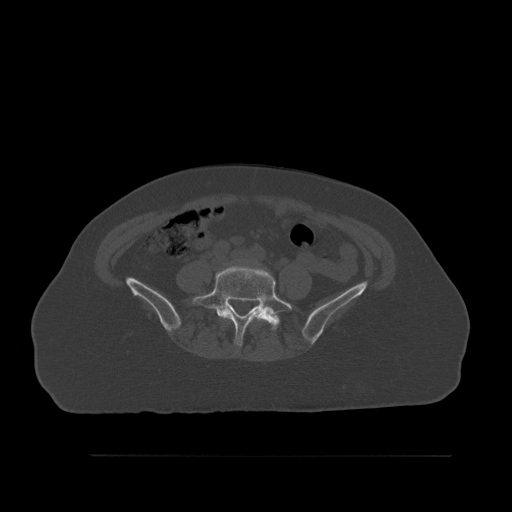
CT including the spine, one axial slice; slice 191 of 527 in the series (ordered by position); bone window (W 1800 / L 400 HU); 1.5 mm slice thickness; 512 × 512 image matrix, field of view 470 × 470 mm. Female patient, age 73 years. From the clinical record (not read from this slice): primary cancer: breast.
Annotated regions visible in this slice (semi-automatically segmented with operator editing):
- L4 vertebra: bounding box (x1, y1, x2, y2) in pixels: (223, 317, 262, 323)
- L5 vertebra: (192, 265, 292, 346)